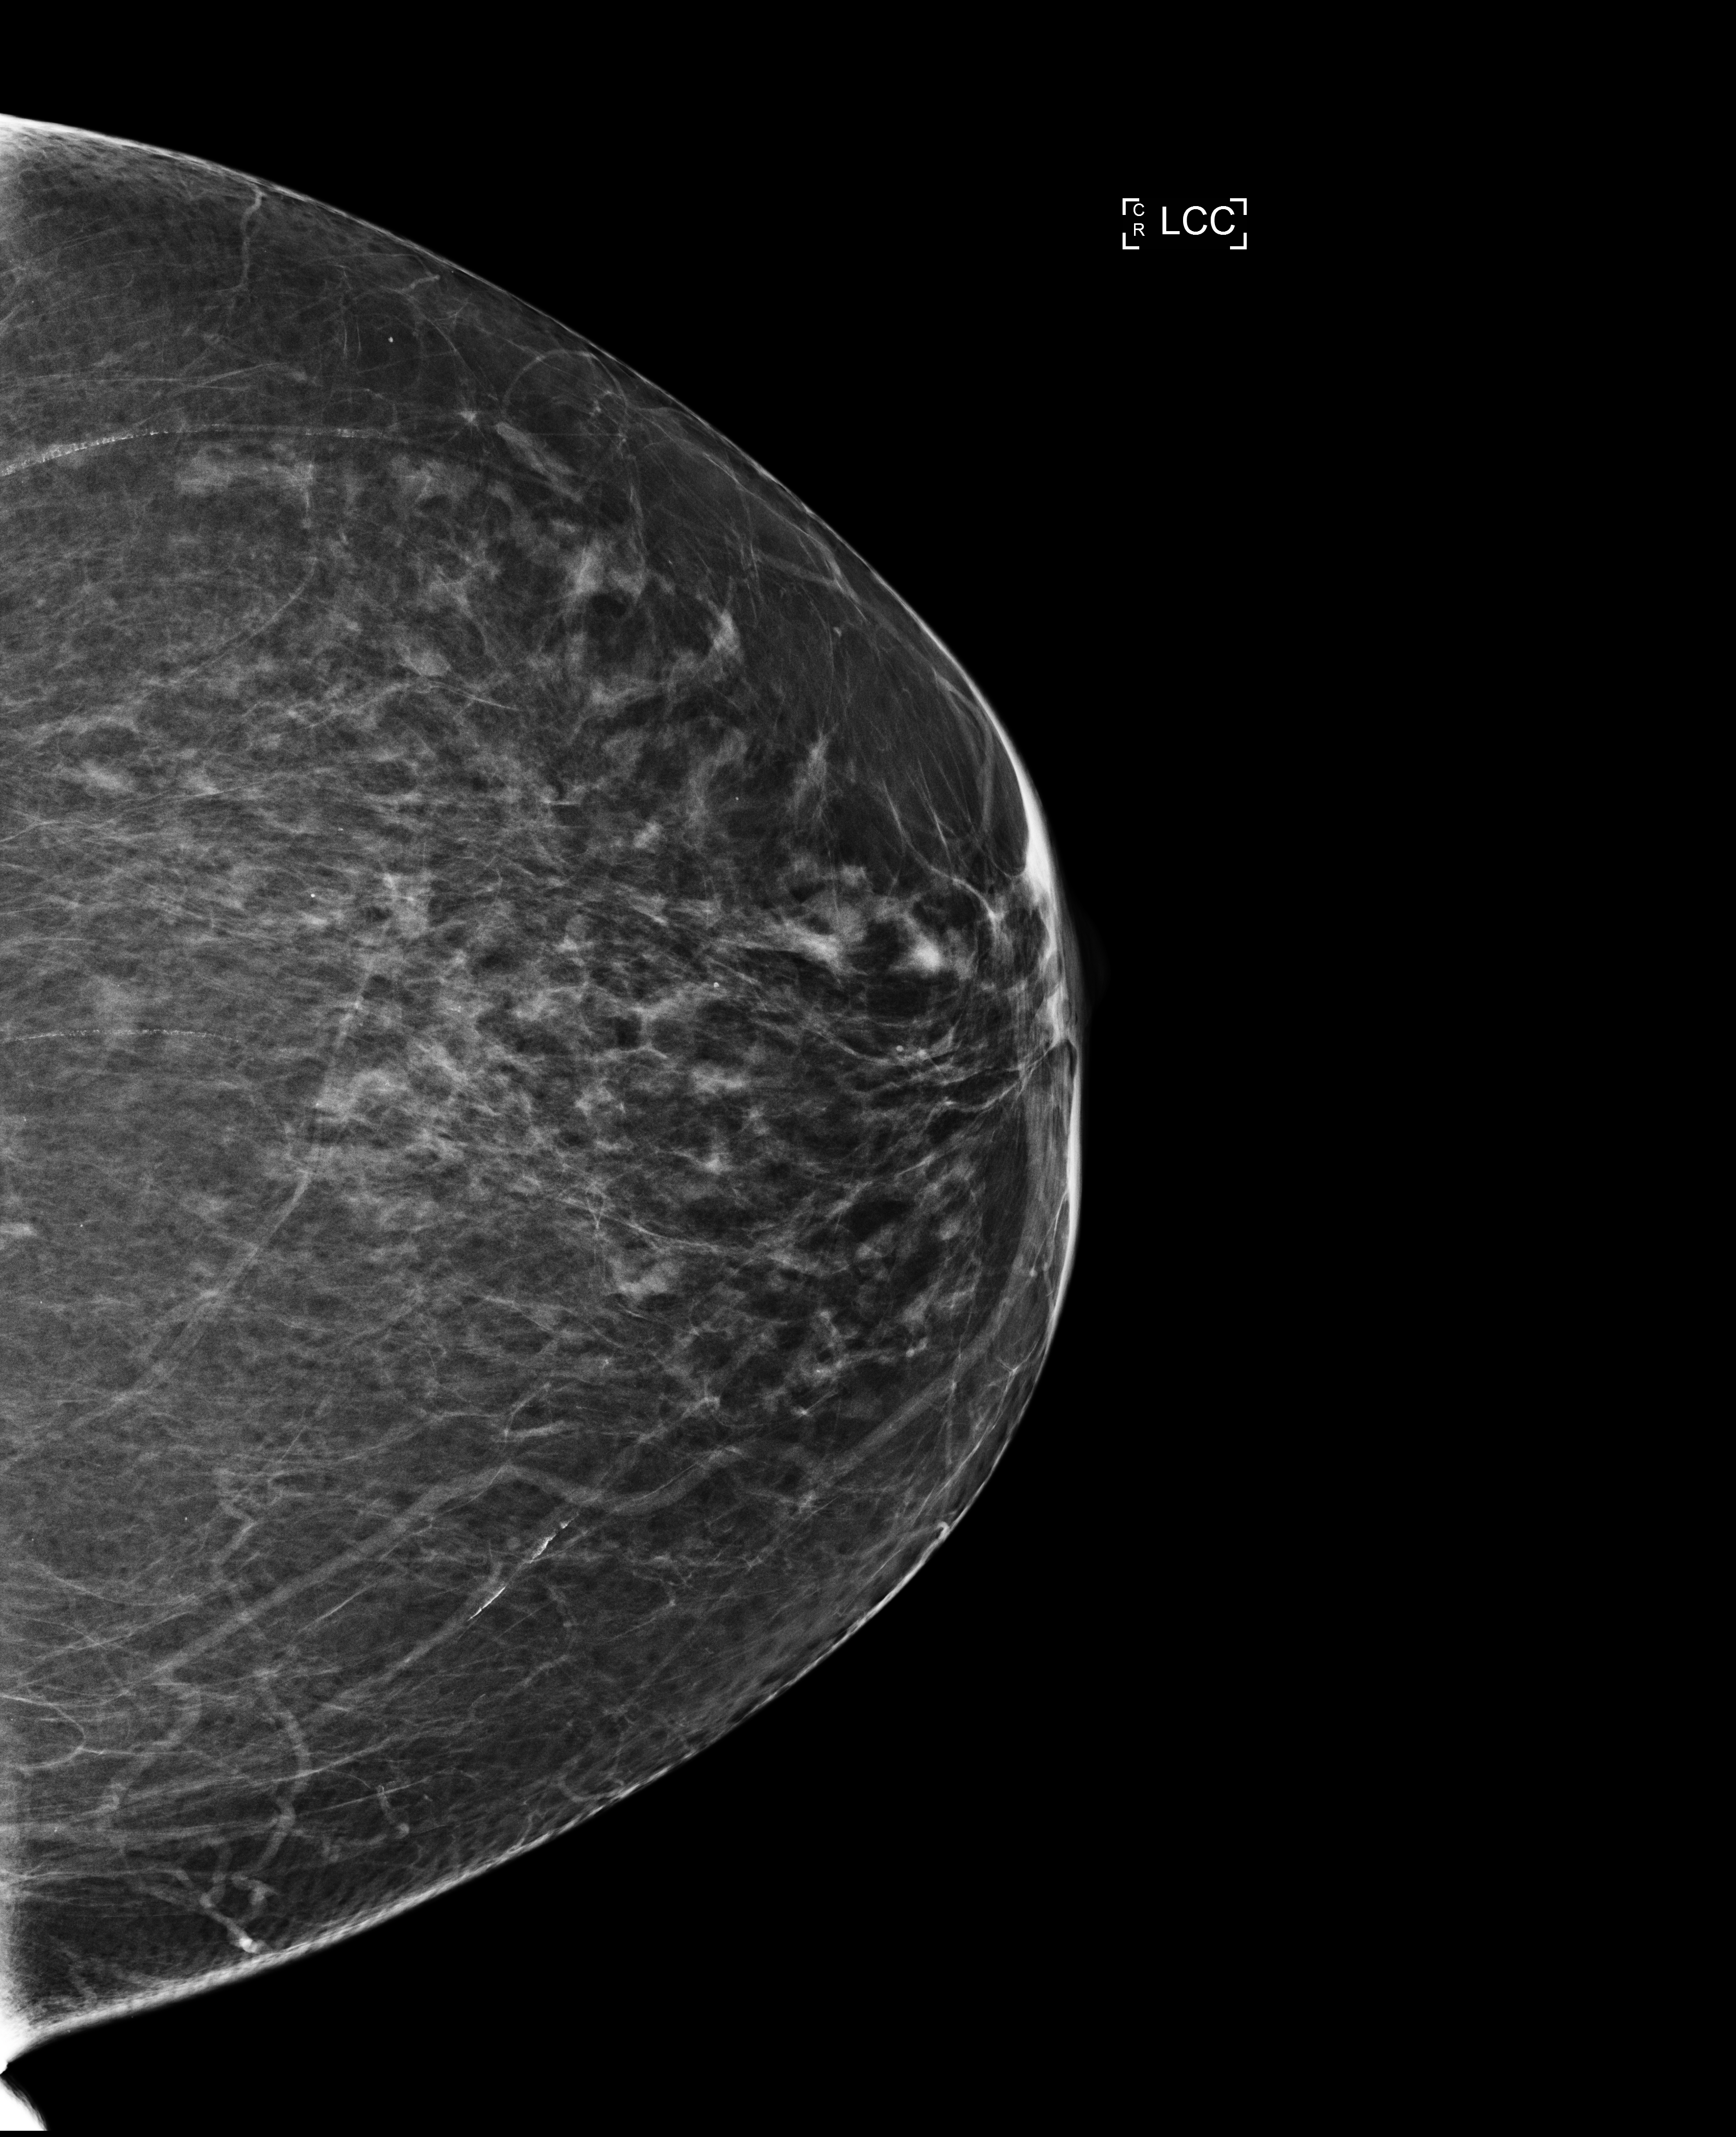
Annual screening mammography examination, compressed breast thickness 62 mm, system: Selenia Dimensions. Patient aged 74 years (female).
Image type: full-field digital mammogram. Breast: left. Projection: CC view.